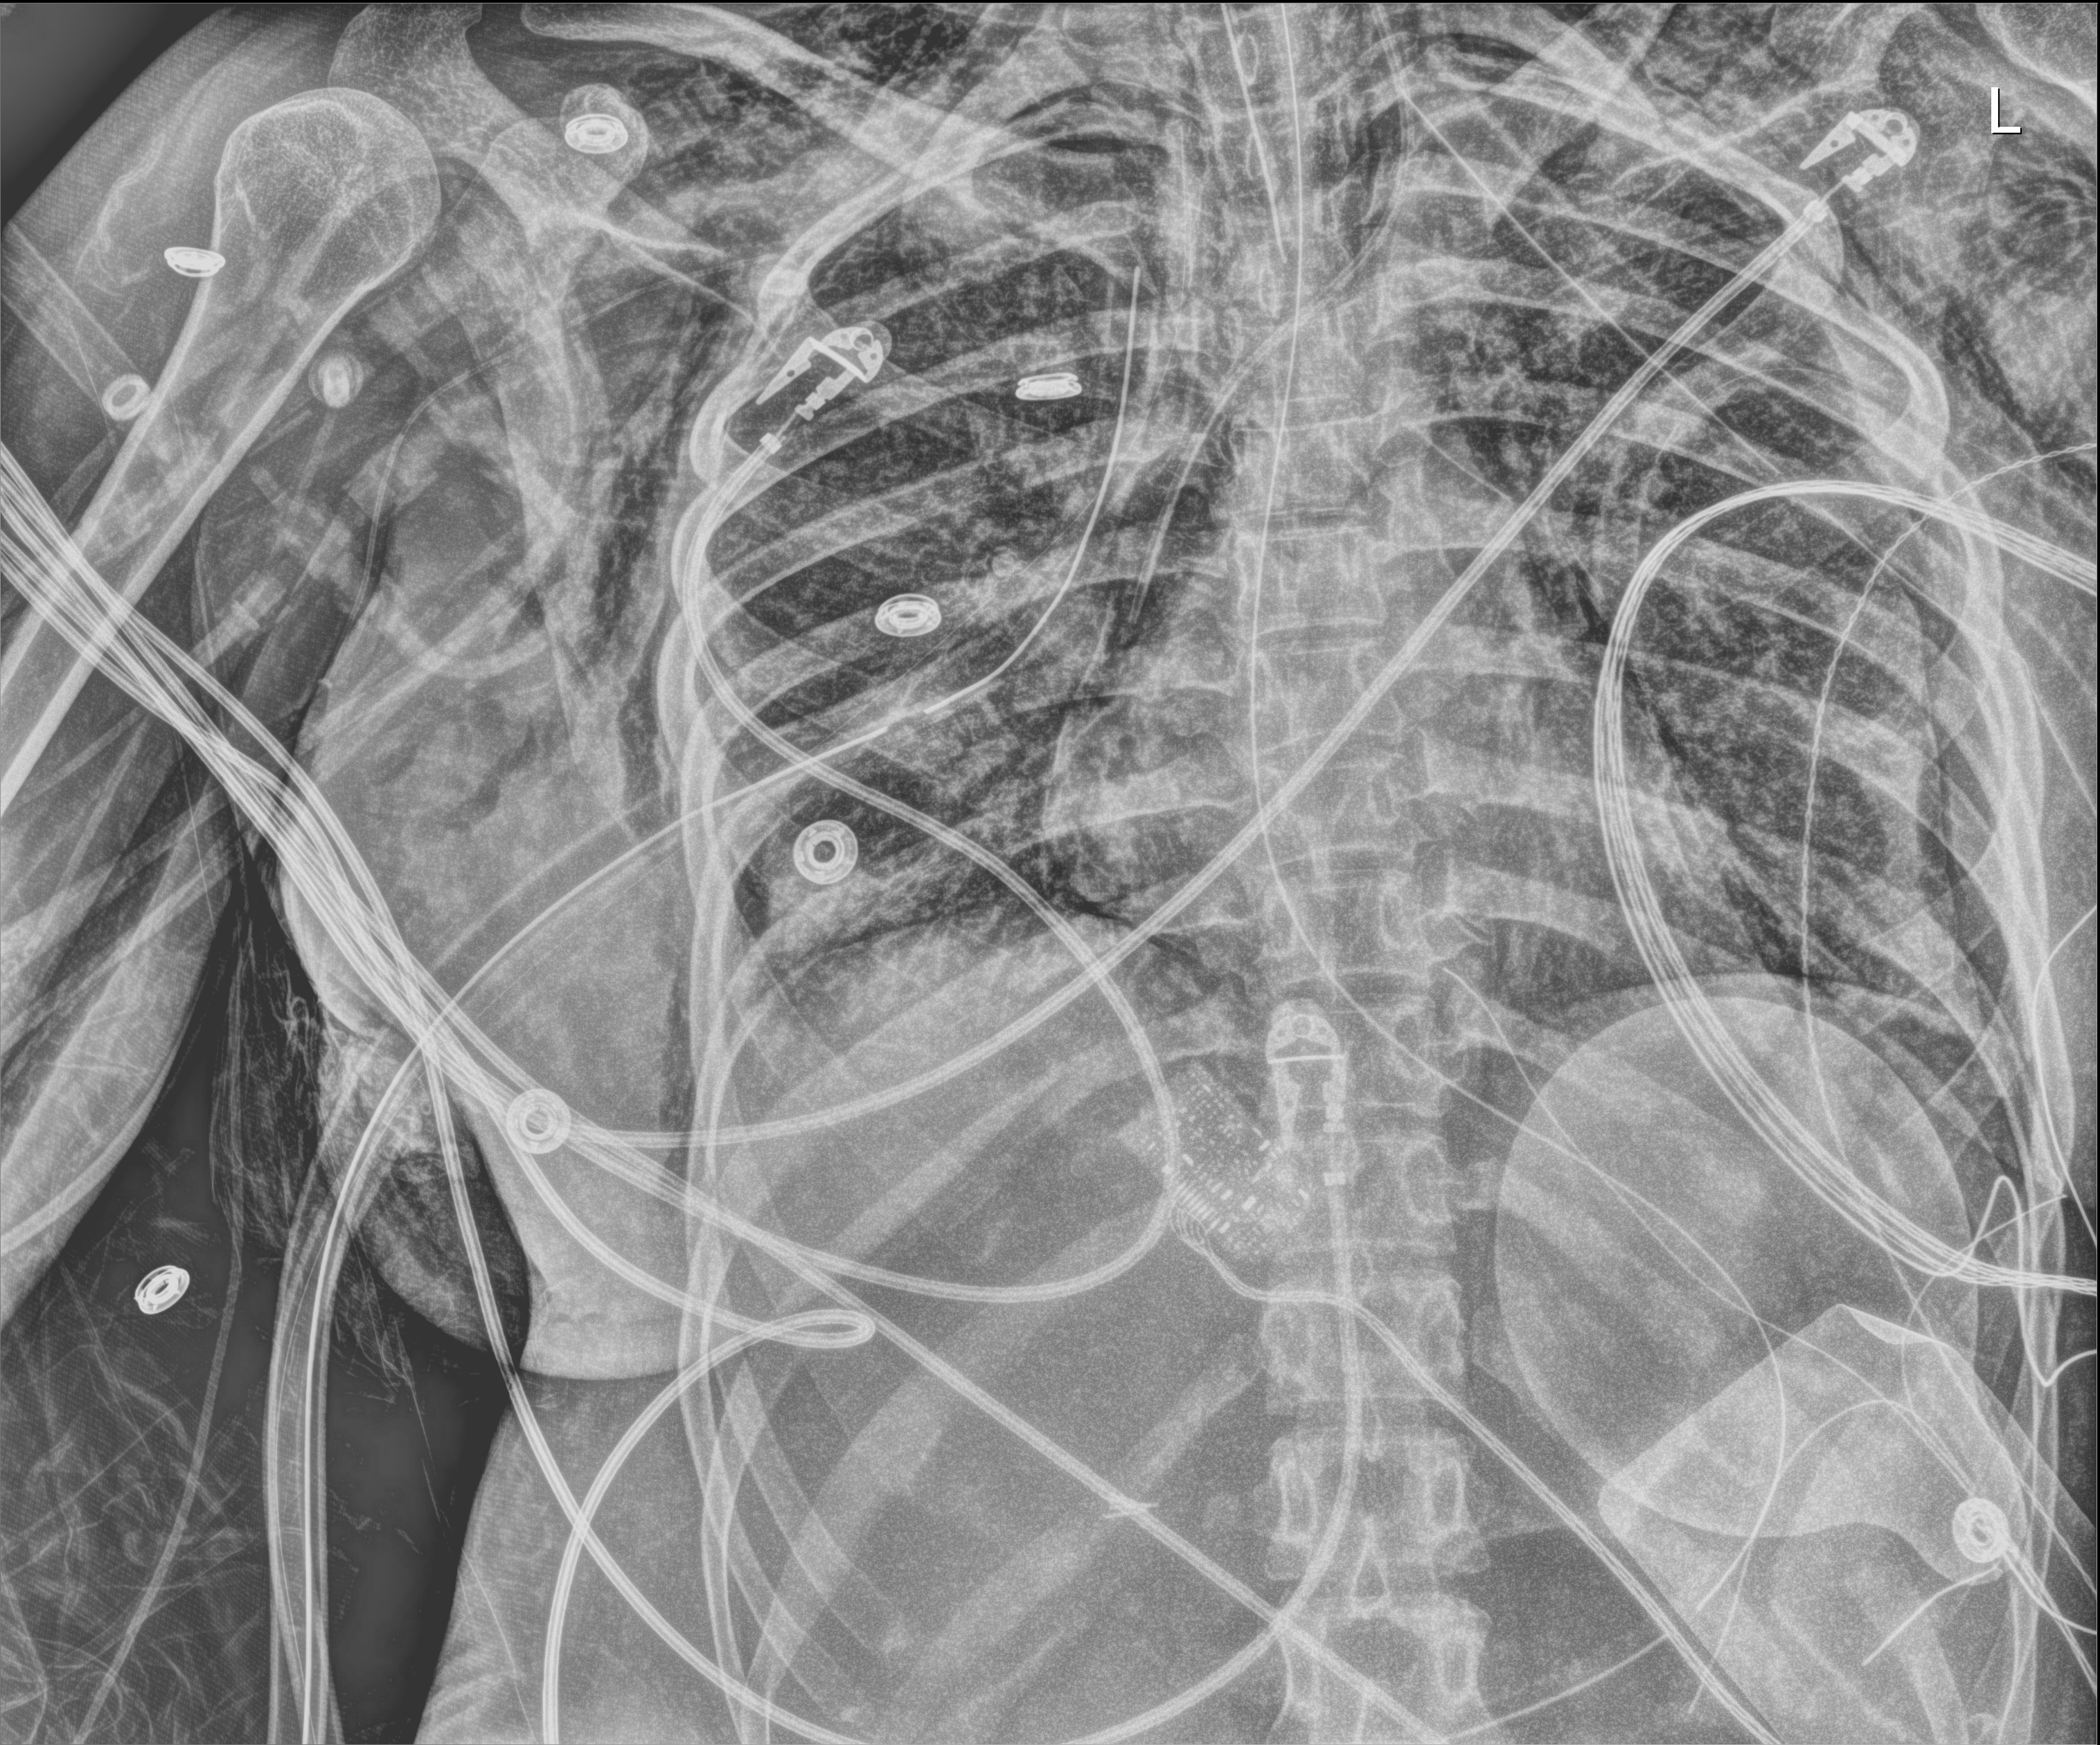
Bedside chest radiograph (digital radiography). Adult patient hospitalised with COVID-19, age 18–59 years.
Hospital-stay facts (about this admission, not read from this image; timing relative to this image not recorded):
- mechanically ventilated during this hospital stay: yes
- chronic kidney disease (admission record): no